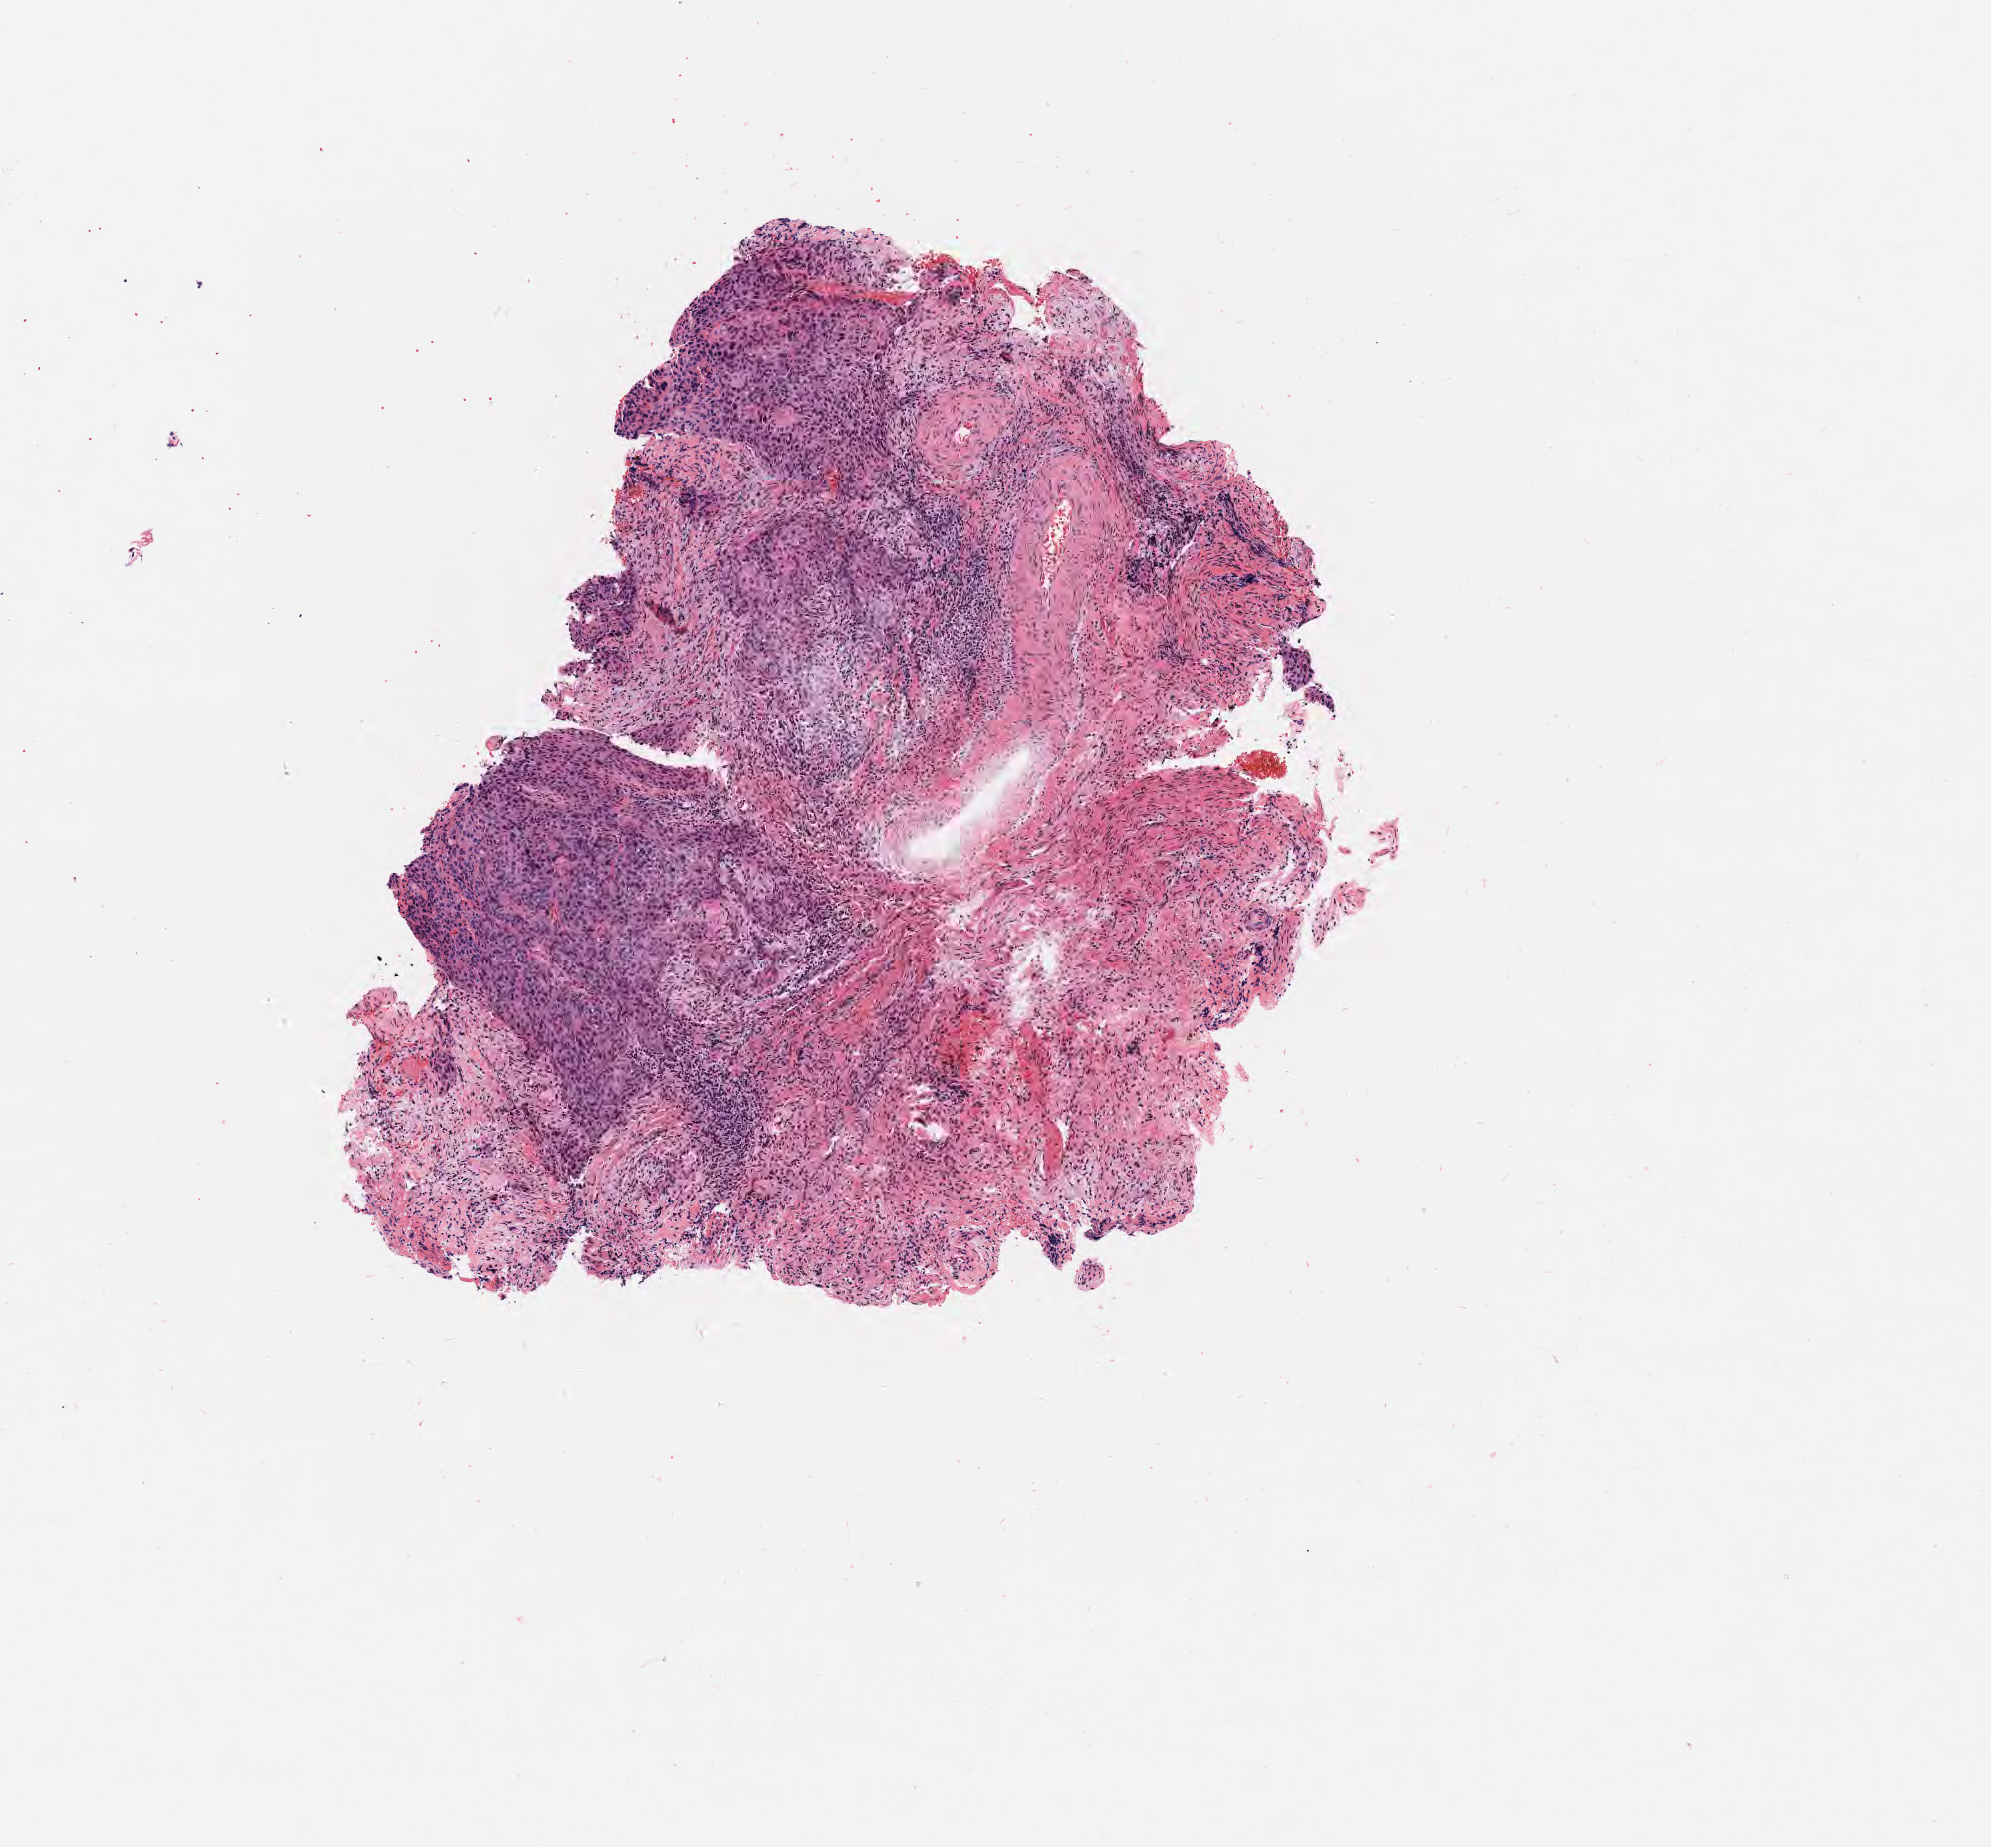
Whole-slide image, haematoxylin and eosin stain, low-resolution overview of the scanned area, about 4.0 x 3.7 mm. Tumor tissue. Site: cervix. Patient female; aged 58.
* histologic diagnosis: Squamous cell carcinoma, large cell, nonkeratinizing, NOS